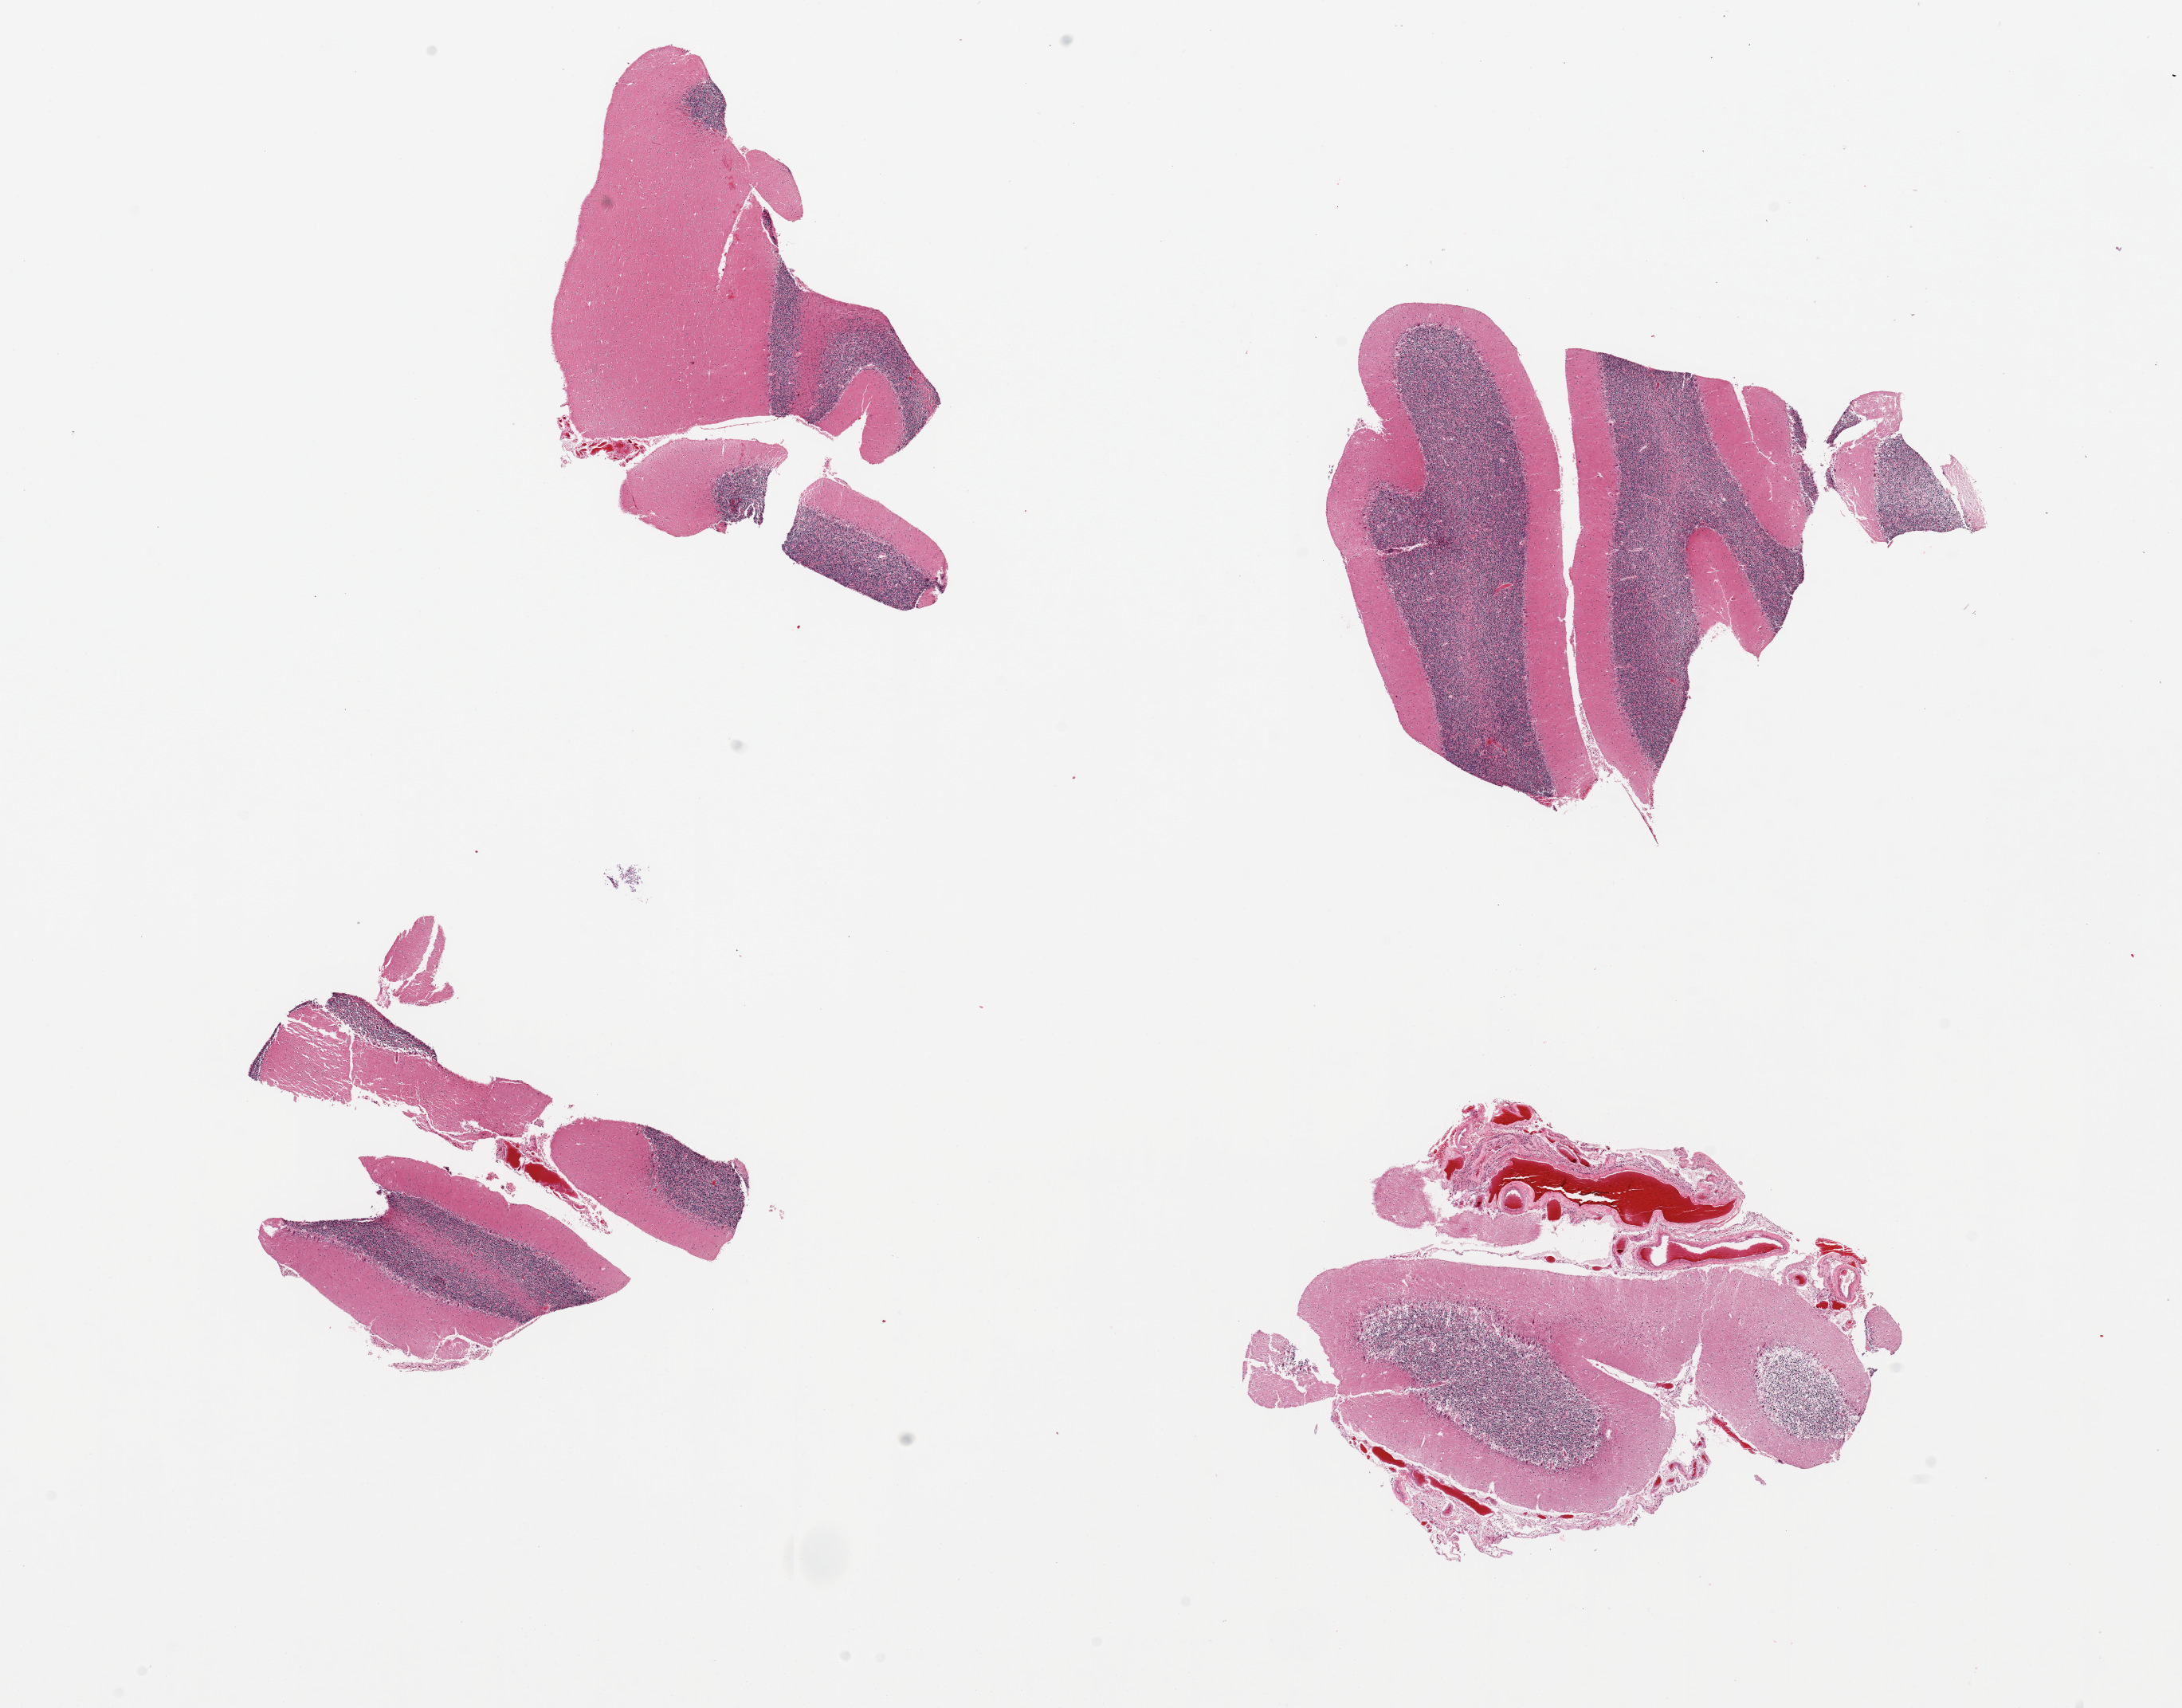
Whole-slide image, H&E stain, a low-resolution overview of the entire scanned area, about 21.7 x 17.0 mm (acquisition: 20x scan); PAXgene-fixed paraffin-embedded (PFPE) section; sampled site (target tissue): cerebellum; donor tissue sample.
Pathologist's review note for this sample: 4 pieces; 1 has adherent meninges.